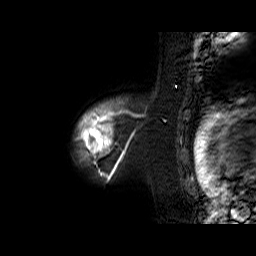
Breast MRI (dynamic contrast-enhanced), one sagittal slice; slice 54 of 60 in the series (ordered by position); dynamic contrast-enhanced series, time point 2 of 6 at this slice position (early post-contrast); 1.5 T; TE 6.3 ms, TR 32.9 ms; 4 mm slice thickness; 256 × 256 image matrix. Female patient. From the clinical record (not read from this slice): setting: breast cancer imaged before/during neoadjuvant chemotherapy; receptor status: triple-negative.
Structures marked on this image (semi-automatically segmented with operator editing):
- analysis volume of interest (the breast-tissue region the enhancement analysis was run in; not a lesion): bounding box <76,100,143,170> (left, top, right, bottom; pixels)
- tumour enhancement mask (voxels above the 100 % enhancement threshold inside the analysis volume of interest): <77,100,132,170>